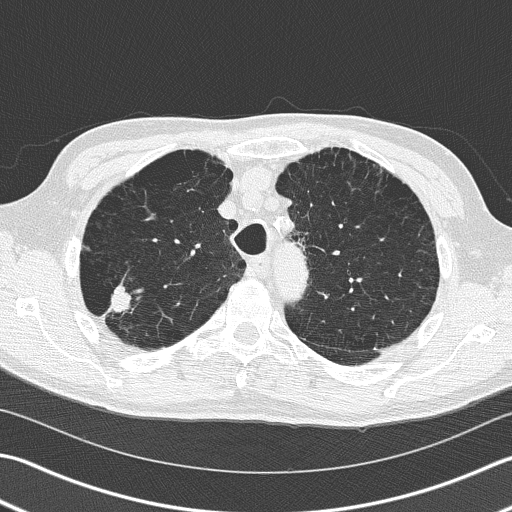
Low-dose screening chest CT, one axial slice; slice 122 of 163 in the series (ordered by position); 120 kVp; lung window (W 1500 / L -600 HU); 2 mm slice thickness; 512 × 512 image matrix, field of view 346 × 346 mm.
Outlined on this slice (outlined manually by an expert reader):
- lesion 1 (tumor, upper lobe of right lung): box from (x=108, y=287) to (x=131, y=314) px